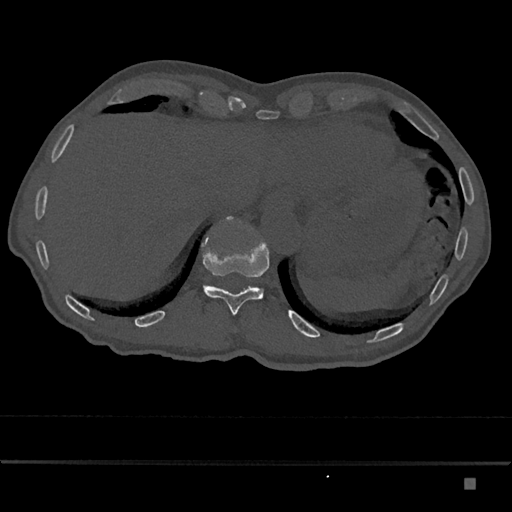
CT including the spine, one axial slice; slice 671 of 797 in the series (ordered by position); reconstruction kernel Br40s/3; bone window (W 1800 / L 400 HU); 512 × 512 image matrix, field of view 390 × 390 mm. Patient: male, 72 years. From the clinical record (not read from this slice): primary cancer: prostate.
Structures marked on this image (semi-automatically segmented with operator editing):
- T11 vertebra: box from (x=202, y=216) to (x=270, y=316) px